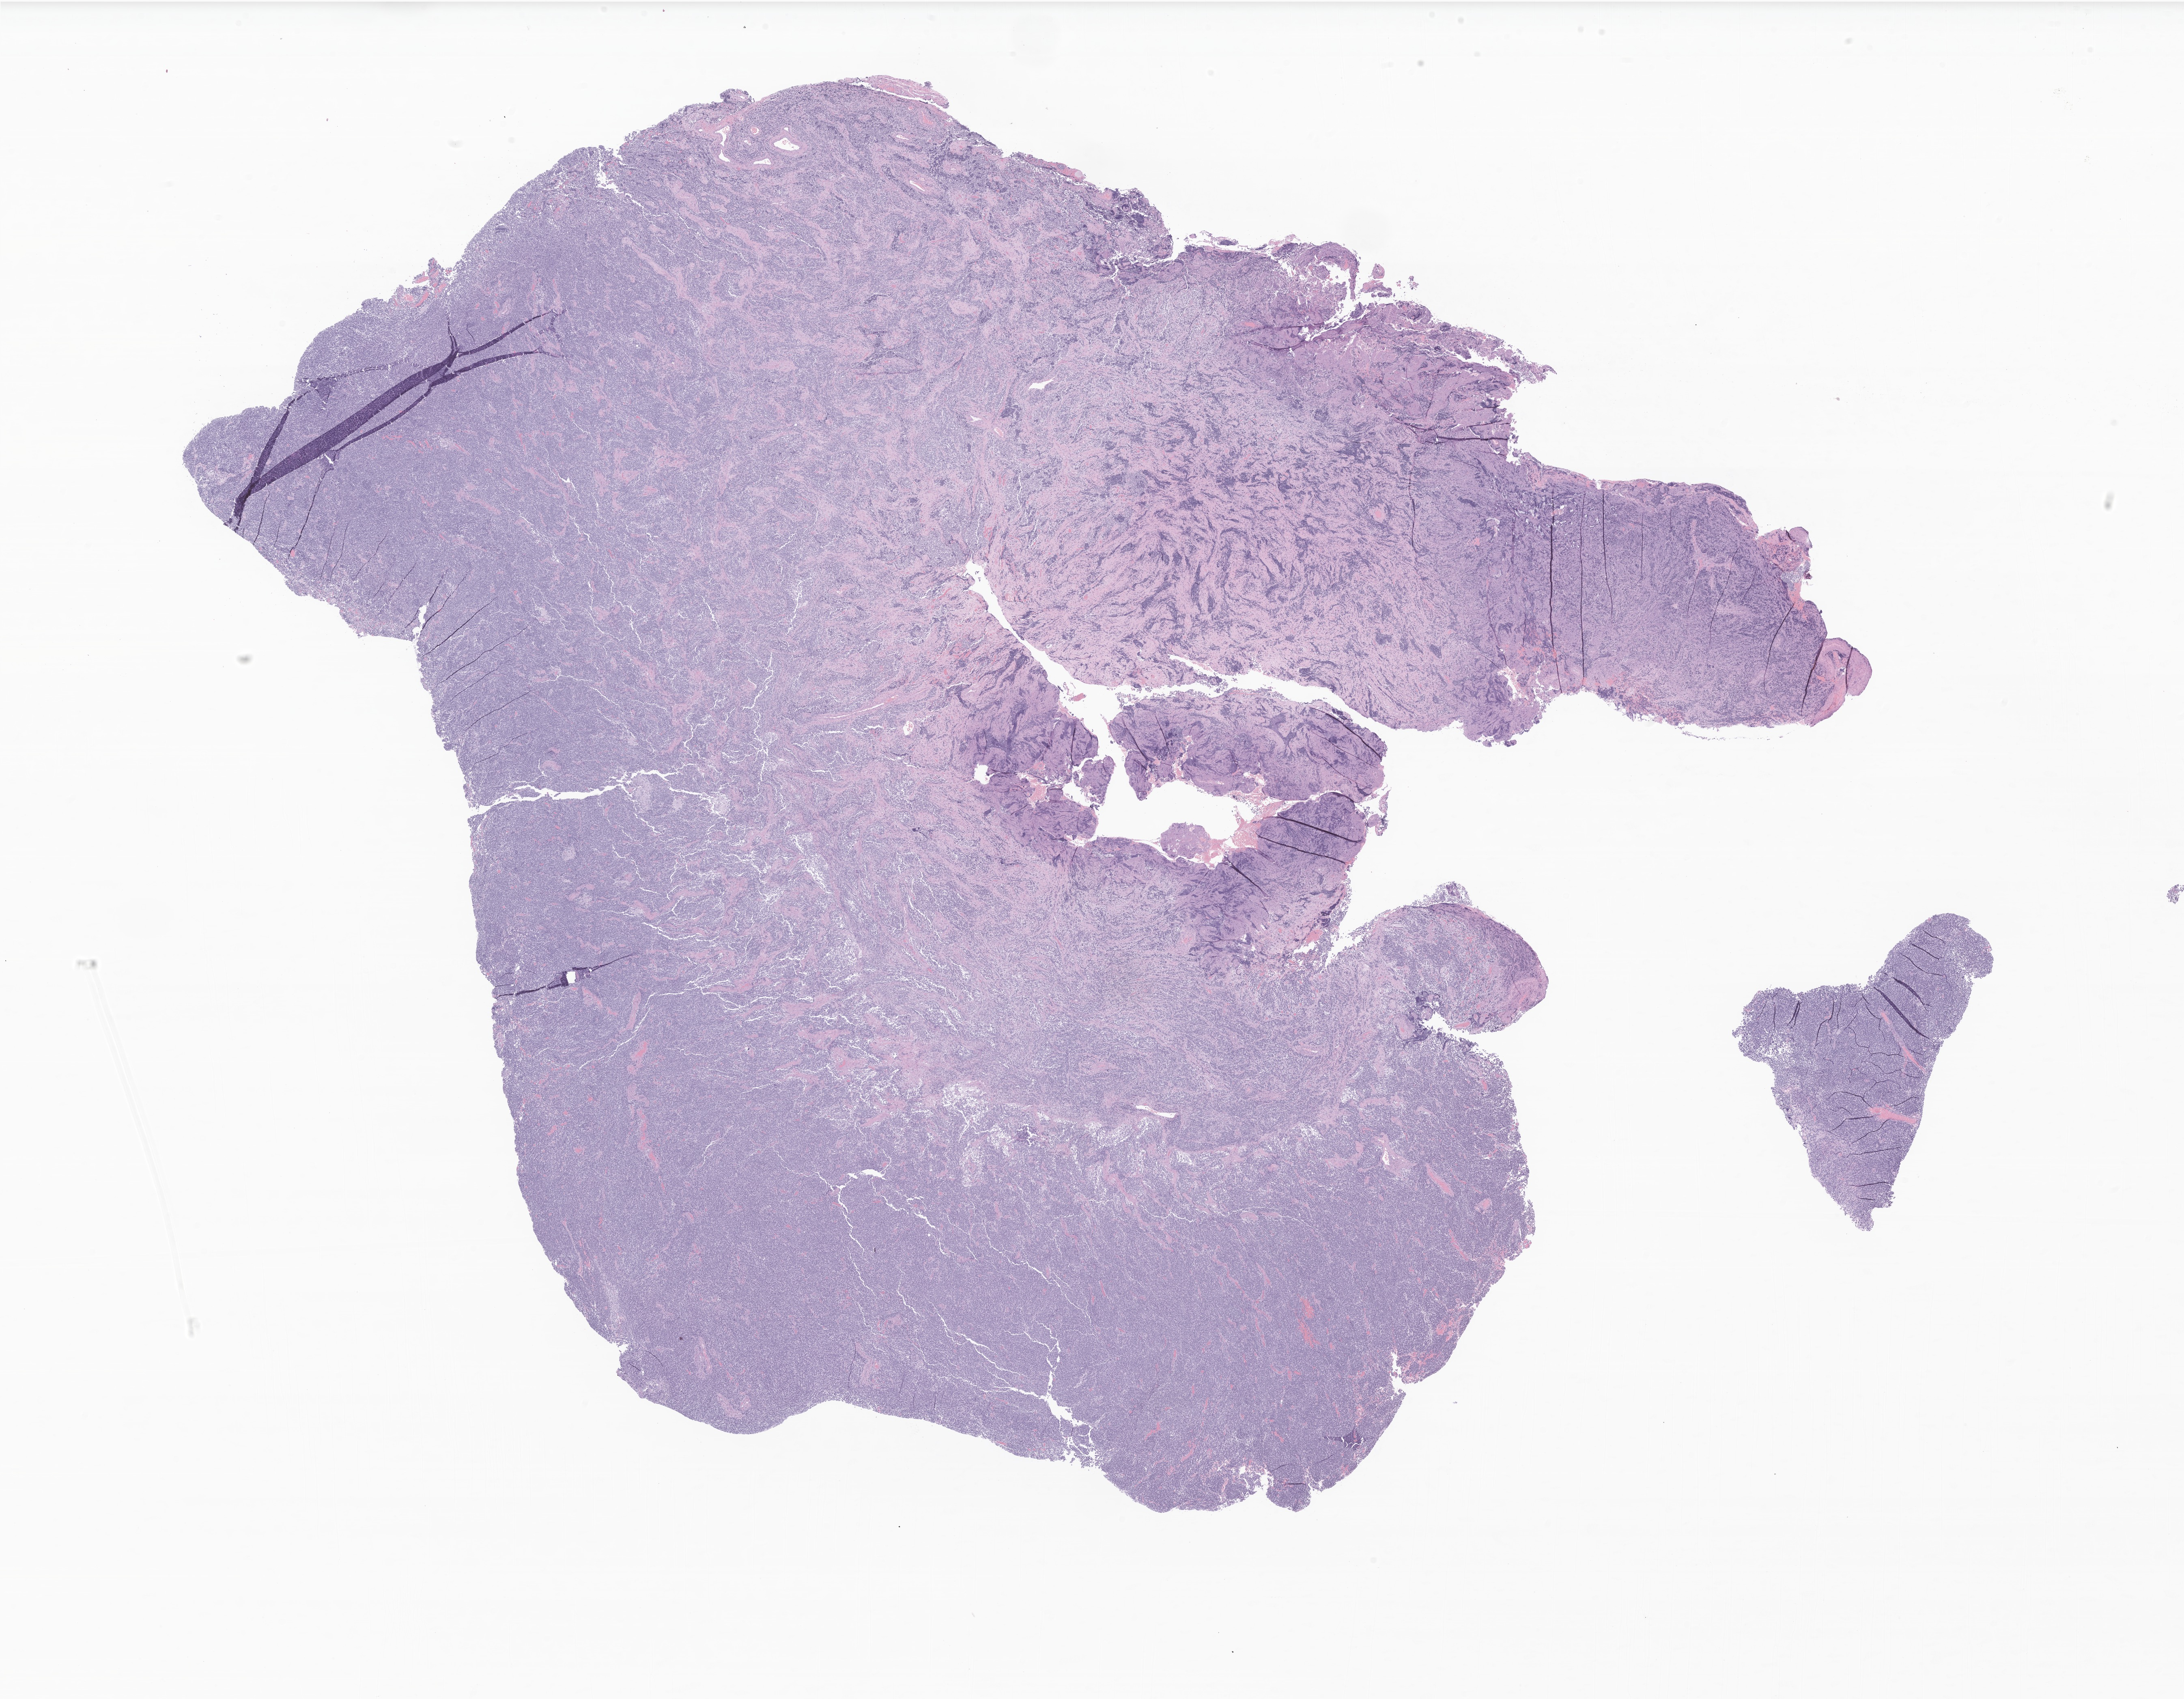
Digitized hematoxylin and eosin (H&E)-stained section of tumor tissue from the brain — low-resolution overview of the scanned area, about 22.7 x 17.7 mm, FFPE section. Patient: male, age 53 months (4 years 5 months).
Diagnosis (ICD-O-3 morphology term): Neoplasm, uncertain whether benign or malignant.